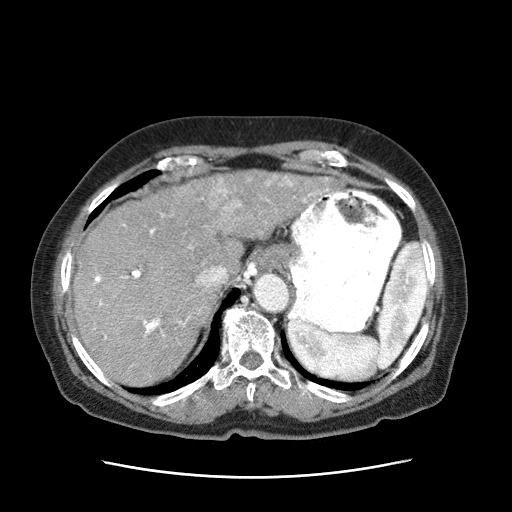
Contrast-enhanced abdominal CT (liver protocol), one axial slice. Slice 51 of 63 in the series (ordered by position). 120 kVp. Intravenous contrast given. Soft-tissue window (W 400 / L 40 HU). 512 × 512 image matrix. Patient: female, 79 years. From the clinical record (not read from this slice): diagnosis: hepatocellular carcinoma (patient treated with transarterial chemoembolisation; whether this scan precedes or follows treatment is not stated here); TNM stage (as recorded): Stage-II; Child-Pugh class: B; tumour nodularity: multinodular; tumour size: 5 cm.
Structures marked on this image (semi-automatically segmented with operator editing):
- abdominal aorta: bounding box <254,274,289,313> (left, top, right, bottom; pixels)
- liver parenchyma outside the tumour (the mass and vessels are separate outlines, so this box may not span the whole liver): <73,182,247,388>
- mass: <191,171,336,241>
- liver vessels: <93,196,295,345>